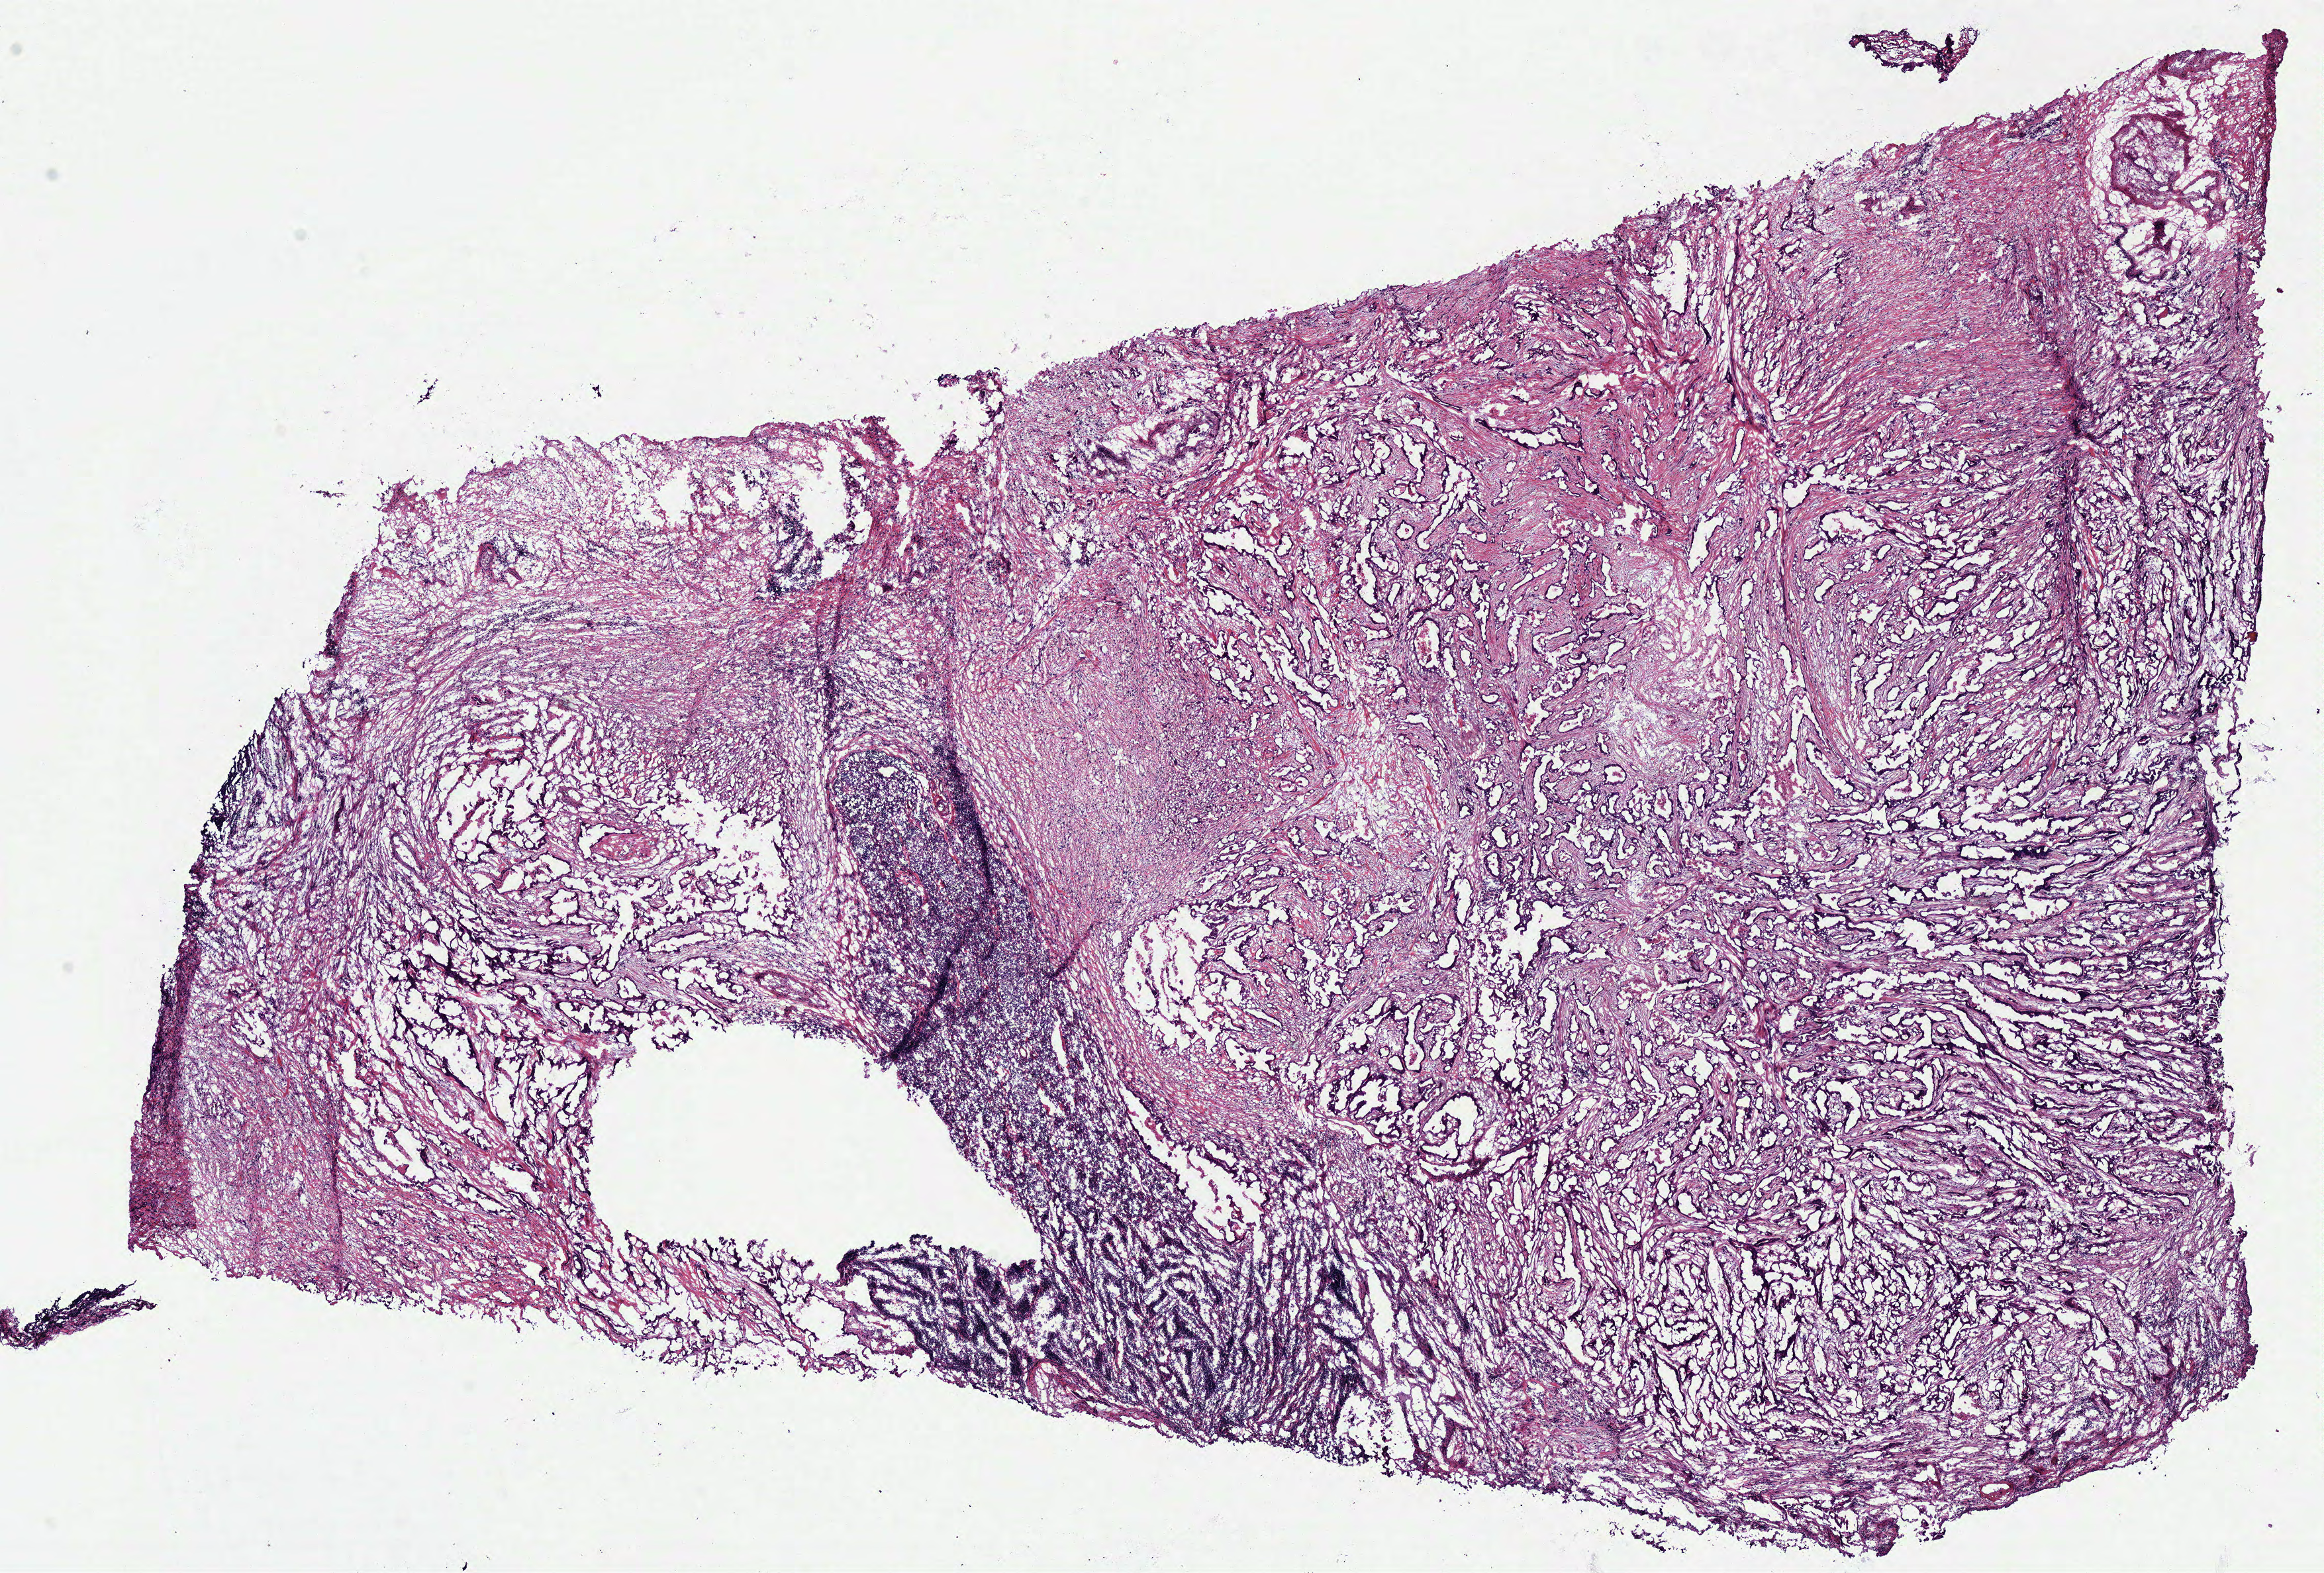
Whole-slide histology image, Hematoxylin and eosin (H&E) stained, low-resolution overview of the scanned area, about 13.8 x 9.4 mm, frozen section from the bottom of the tissue portion, stomach, primary tumour sample. Male patient; age at initial diagnosis 58 years. Histologic grade: G2 (moderately differentiated). Composition of this section per pathologist review: tumour cells 80%, tumour nuclei 75%, normal cells 0%, stromal cells 20%, necrosis 0%.
• pathologic diagnosis: Adenocarcinoma, NOS (cardia, NOS)
• AJCC pathologic stage: II (6th edition)